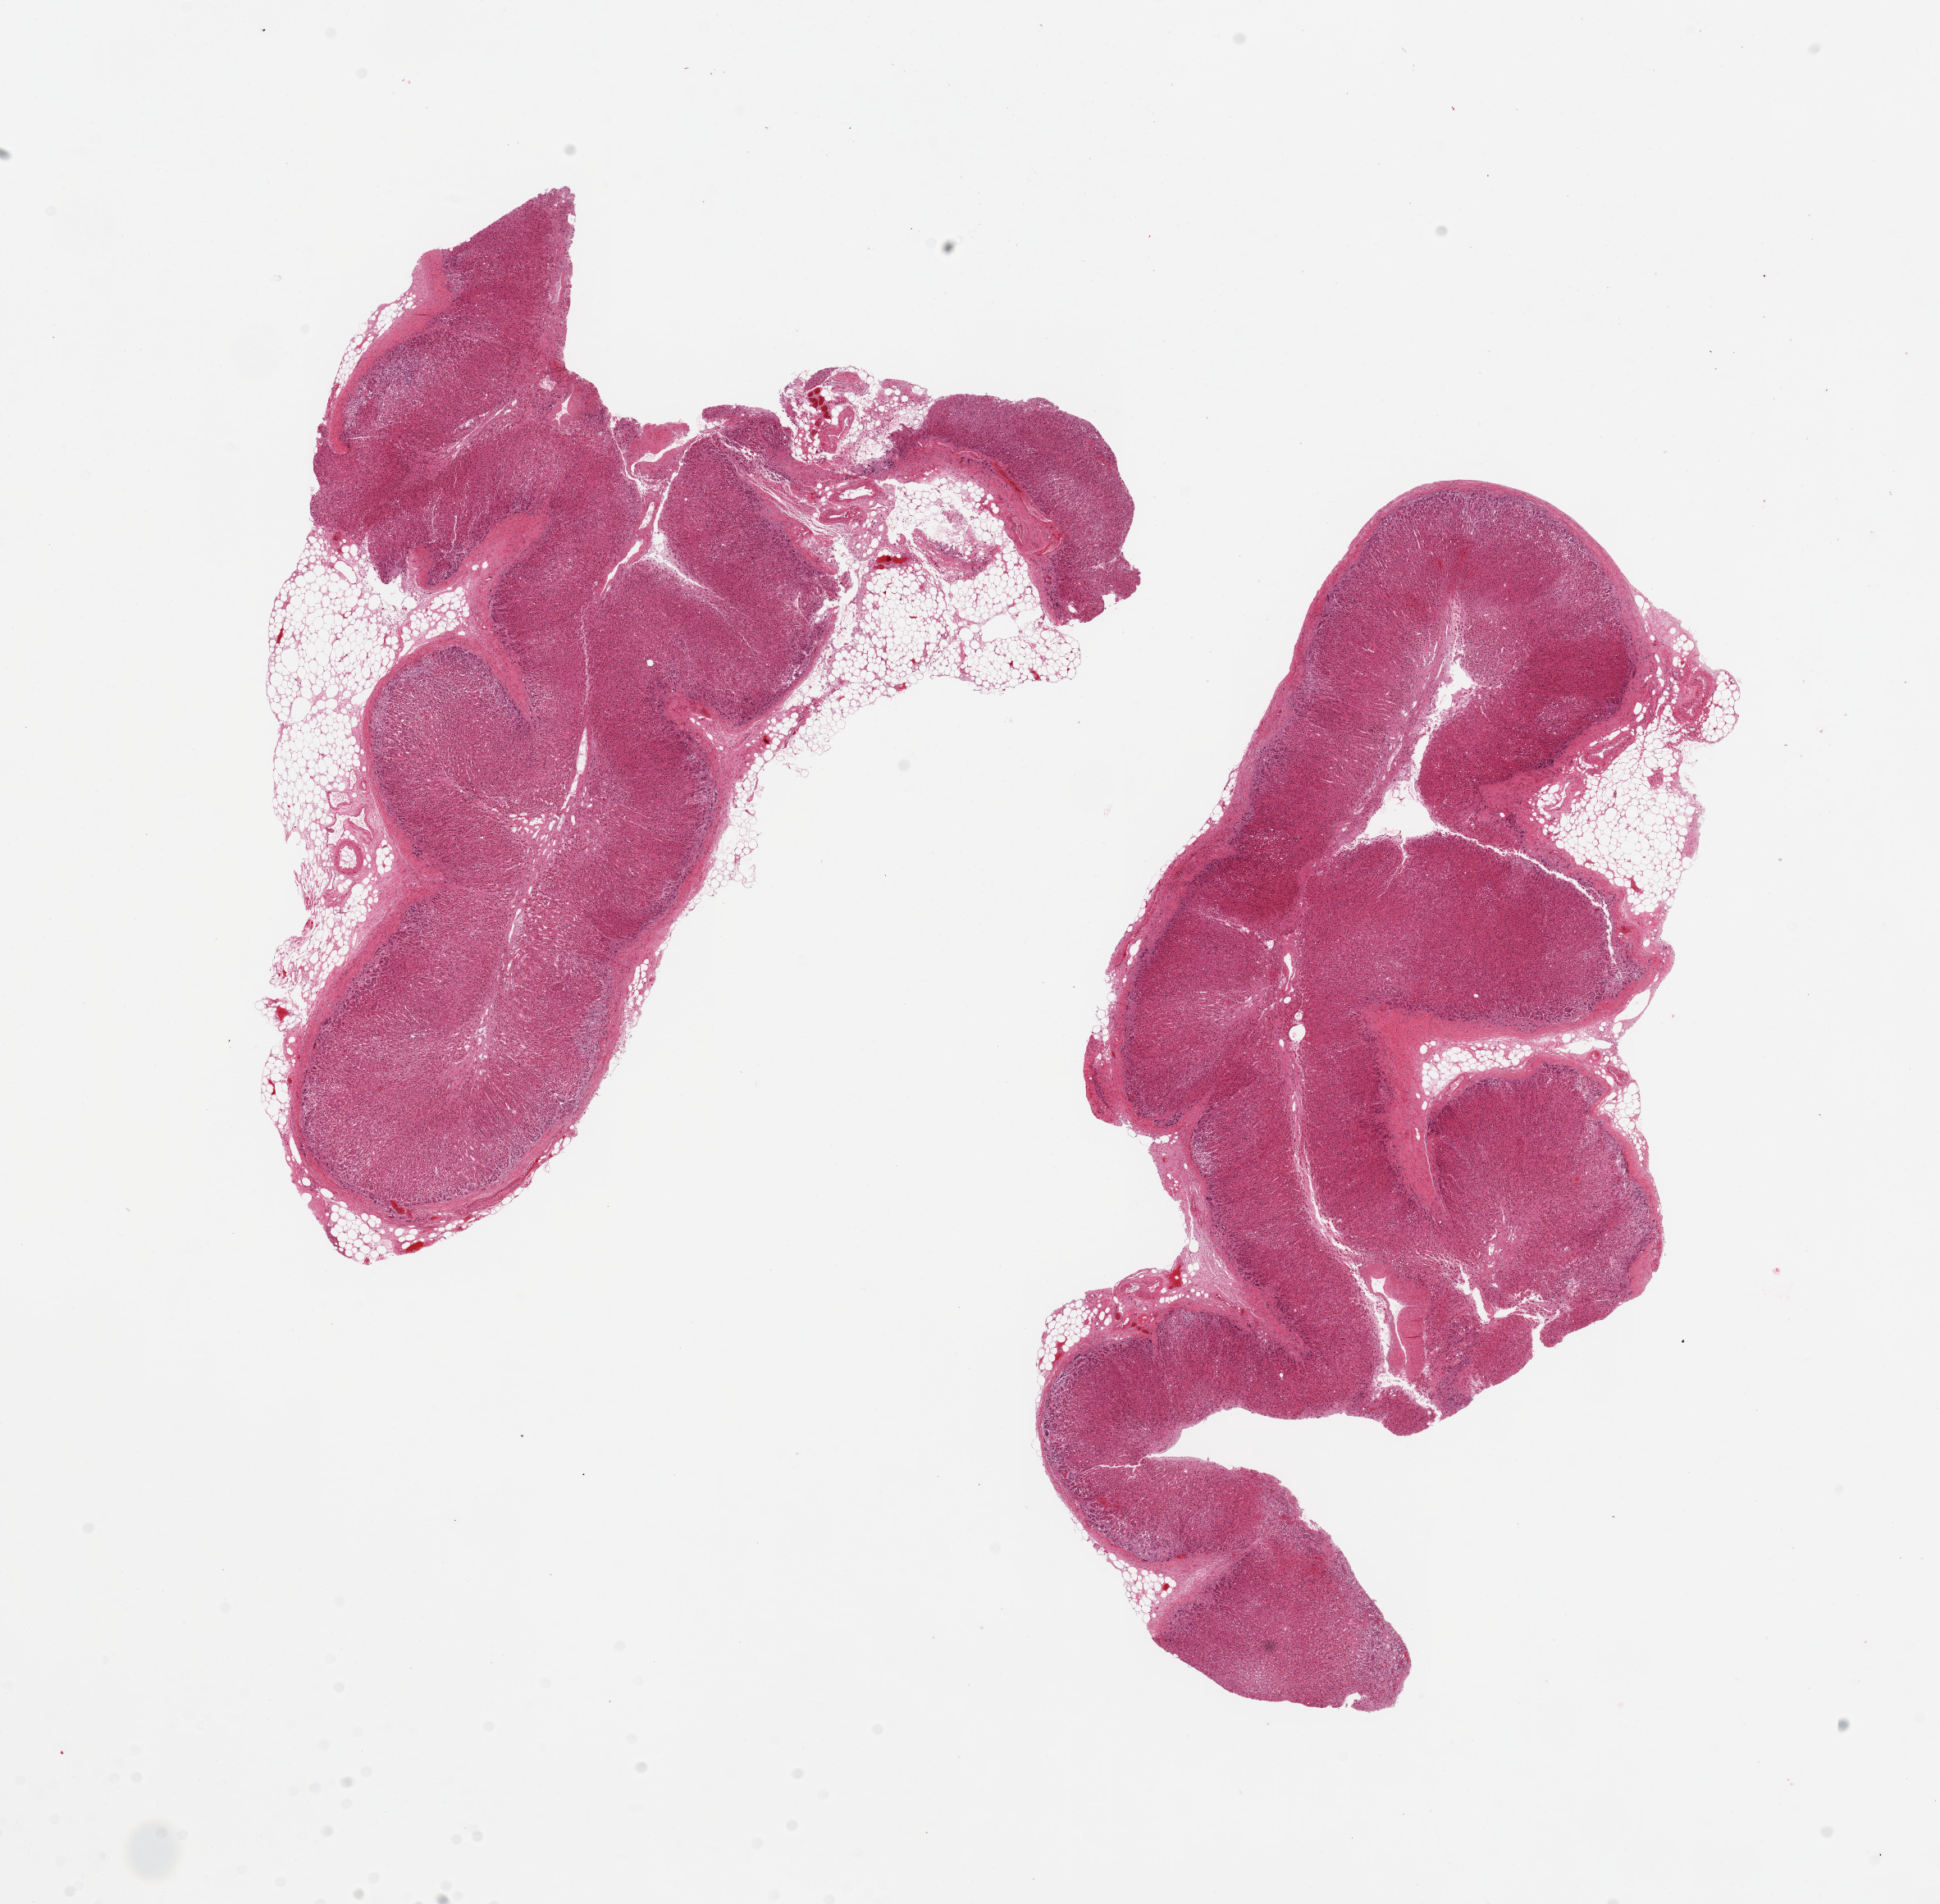
Haematoxylin and eosin whole-slide image — shown as a low-resolution overview of the whole scanned area (about 18.7 x 18.4 mm, acquisition: 20x scan); PAXgene-fixed, paraffin-embedded tissue; target tissue: adrenal gland; tissue donor sample. Donor: female.
Reviewer comment on this tissue sample: 2 pieces; 20% external fat.